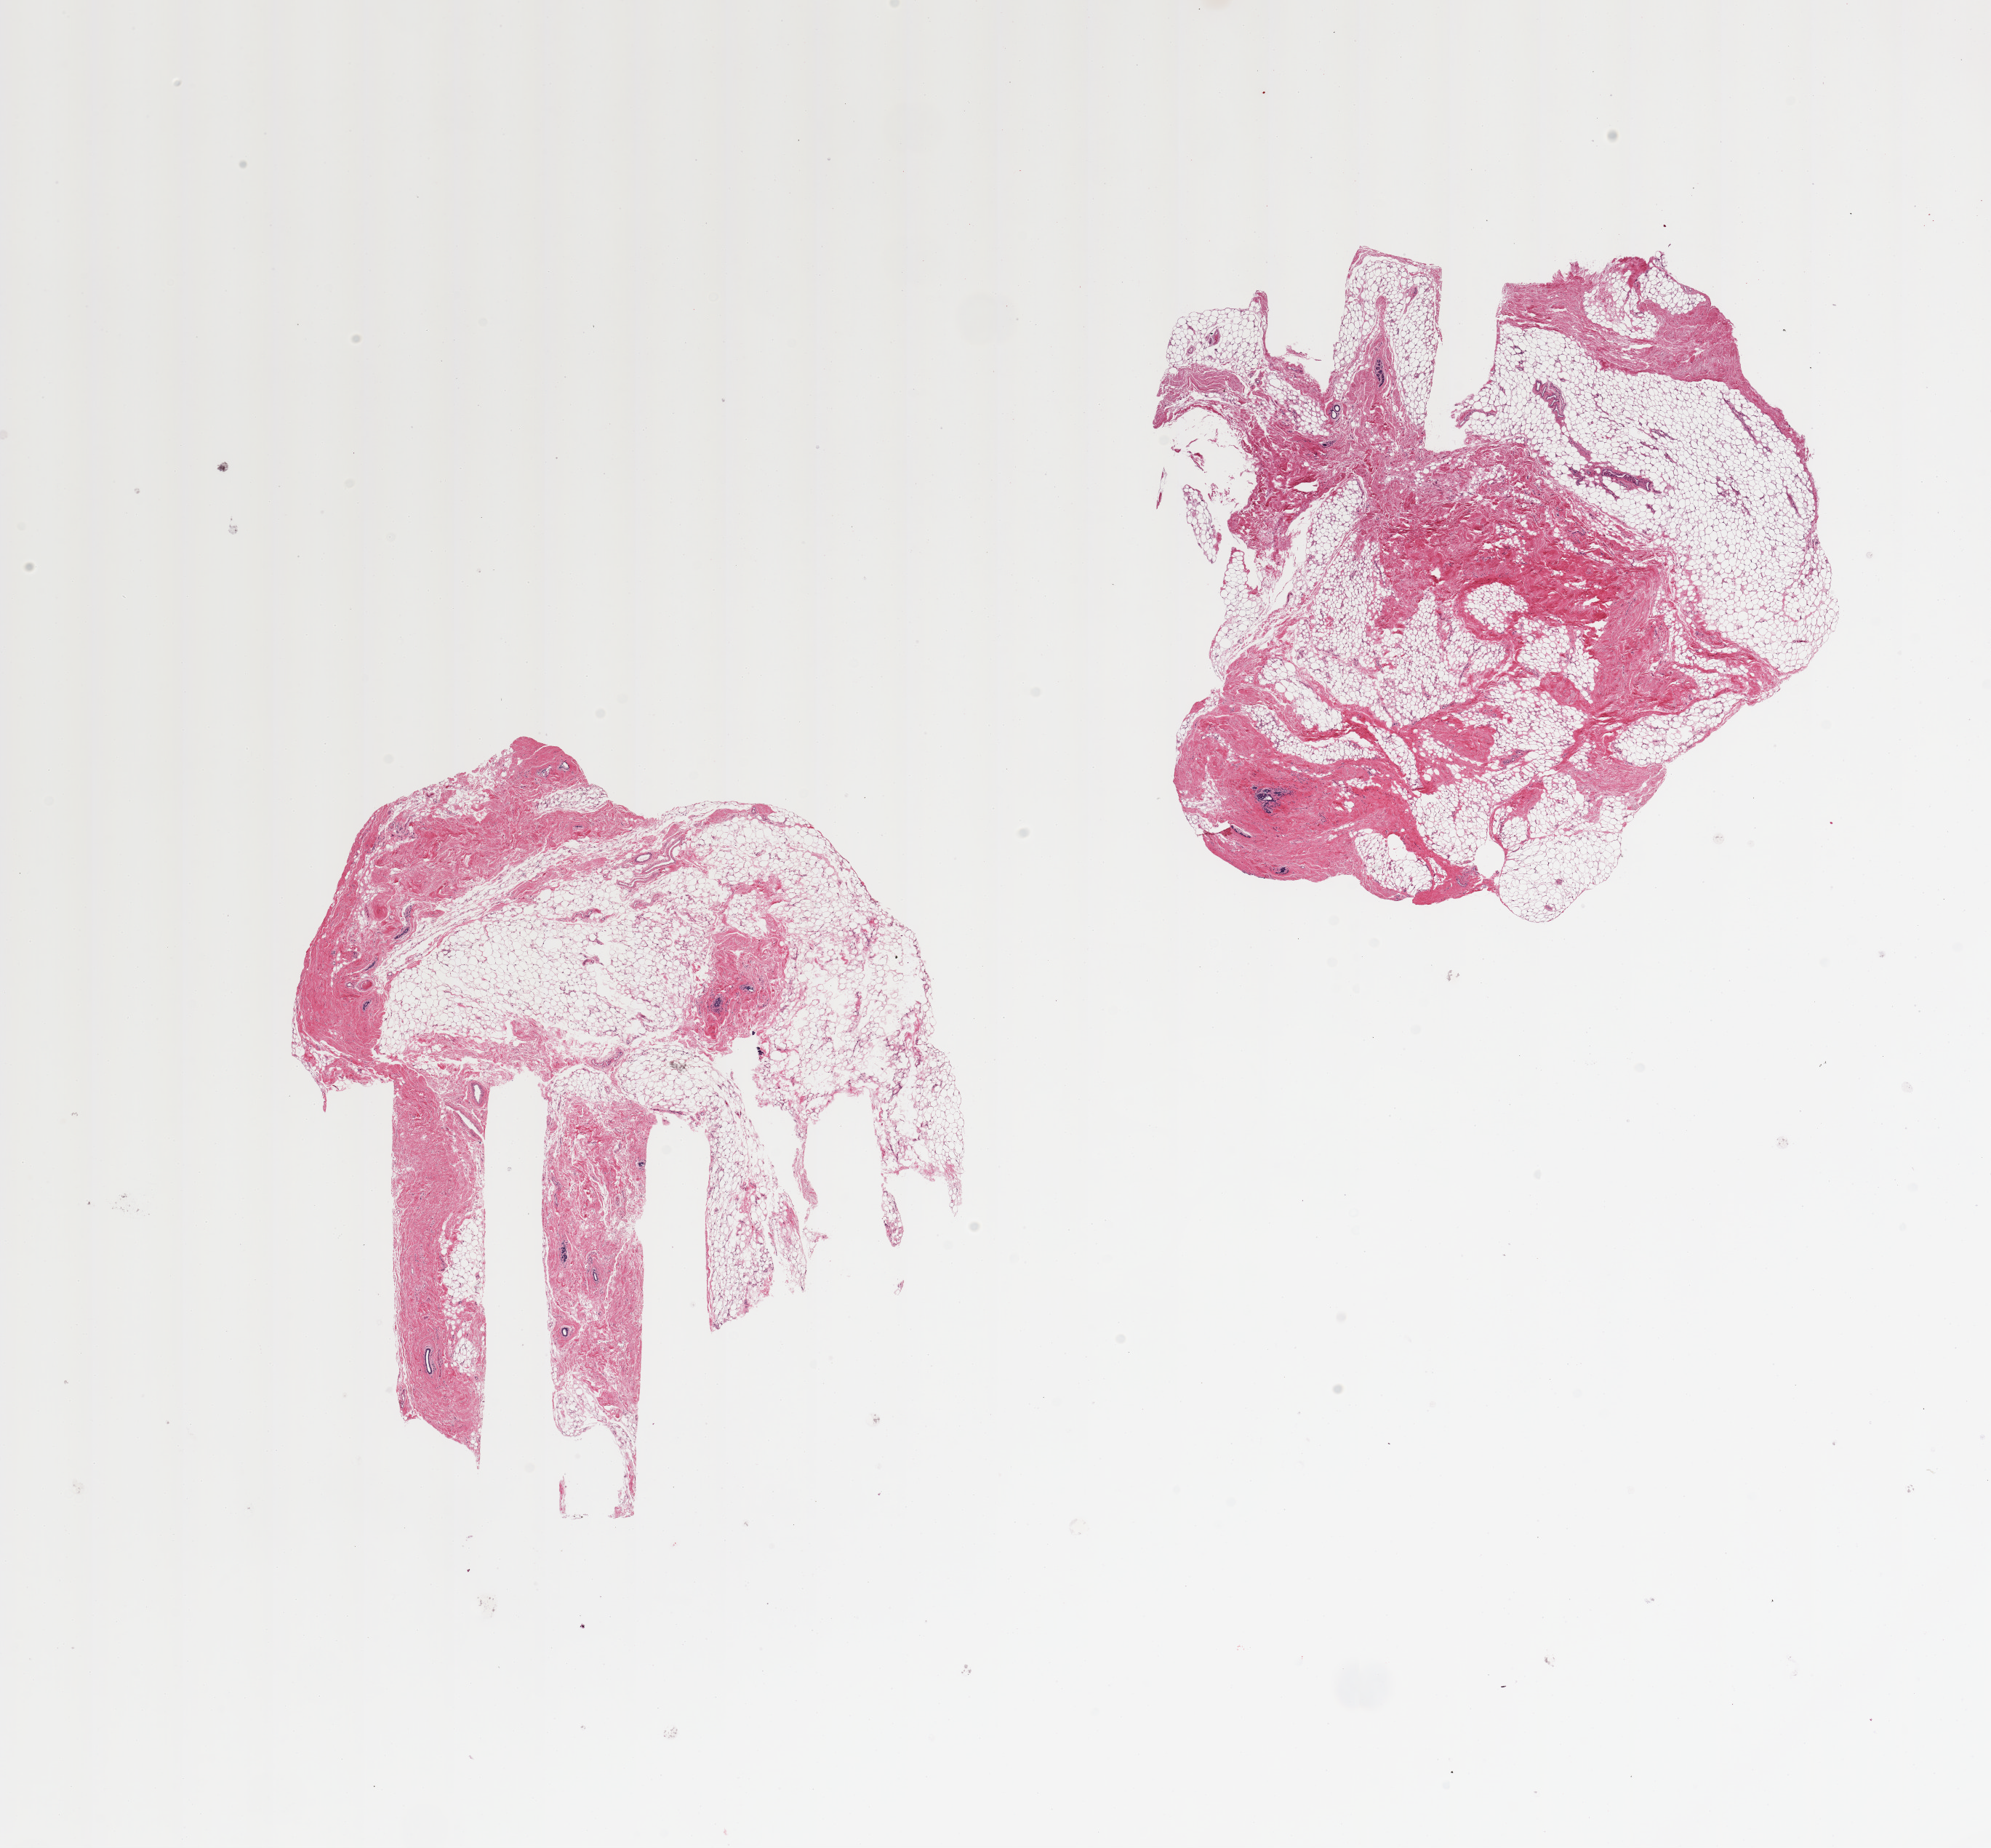
Hematoxylin and eosin (H&E) whole-slide image — whole scanned area (about 21.7 x 20.1 mm) shown as a low-resolution overview, PAXgene-fixed paraffin-embedded (PFPE) section, section of breast (target tissue), donor tissue sample. Donor: female.
* pathologist's review note for this sample: 2 pieces, trace ductal elements